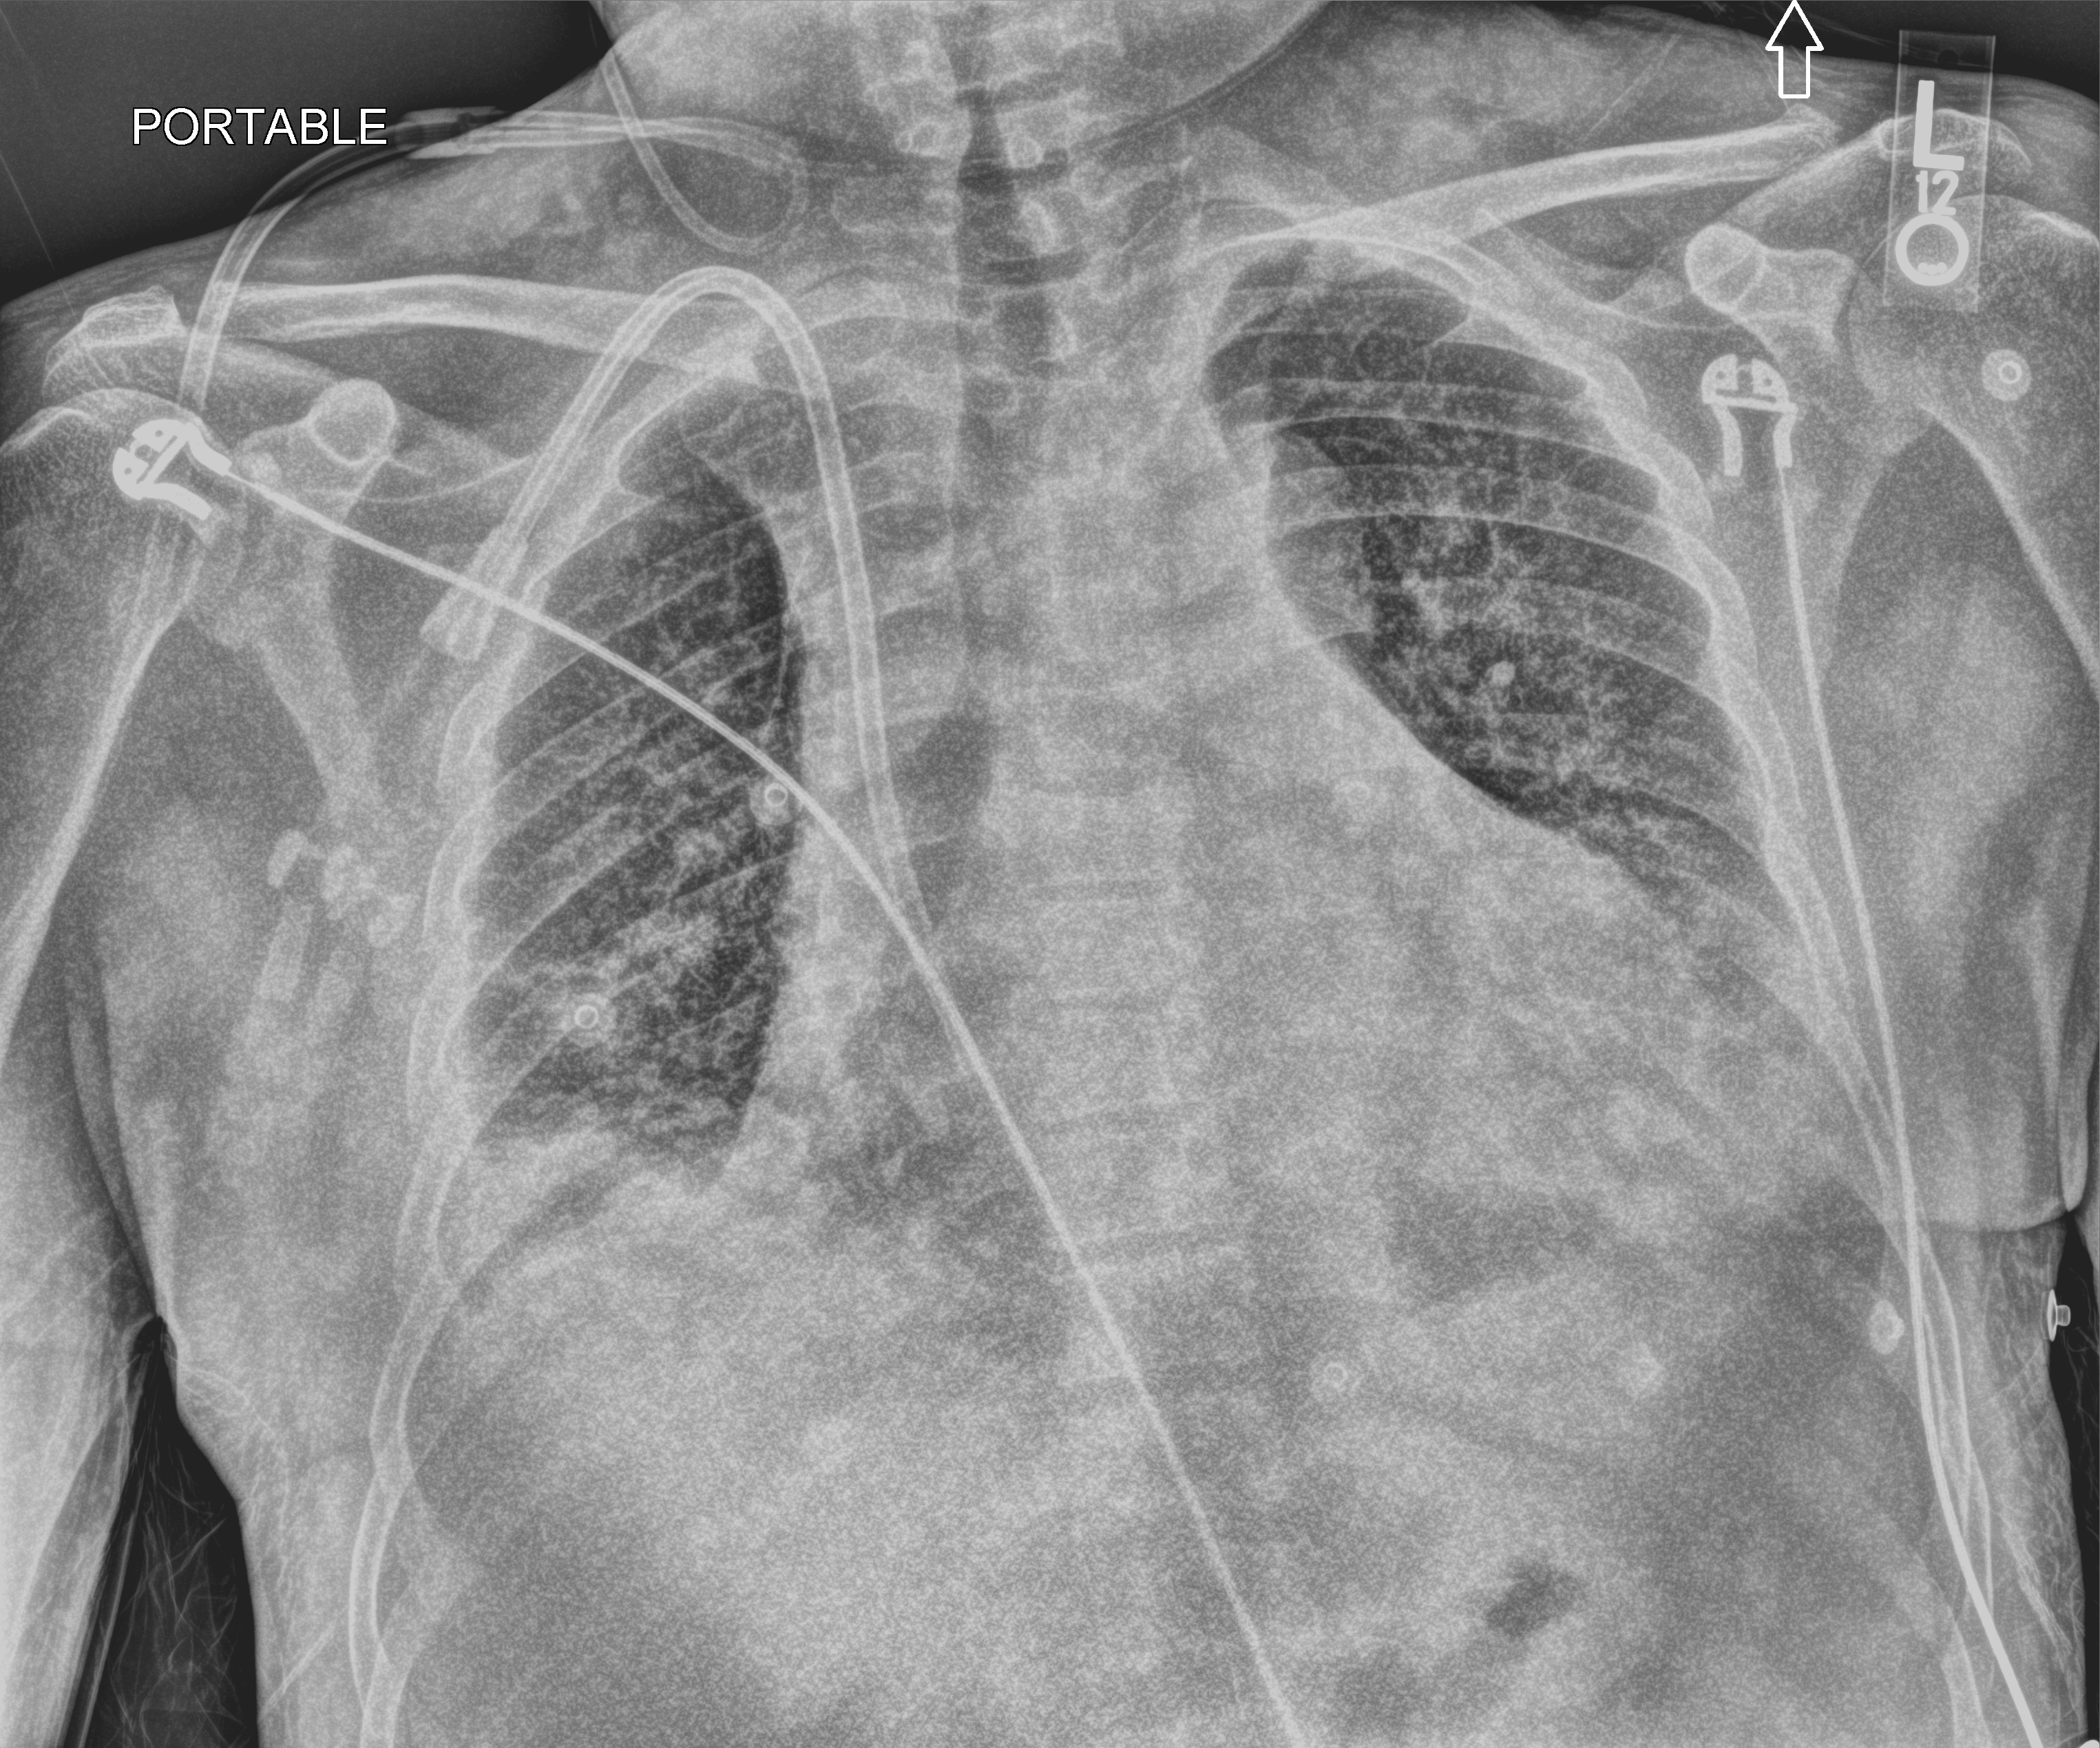
Bedside chest radiograph (computed radiography), anteroposterior (AP) projection. Patient hospitalised with COVID-19; male, aged 18–59 years.
From the hospital-stay record, not from the radiograph (when in the stay this image was taken is not recorded): admitted to intensive care during this hospital stay: no.